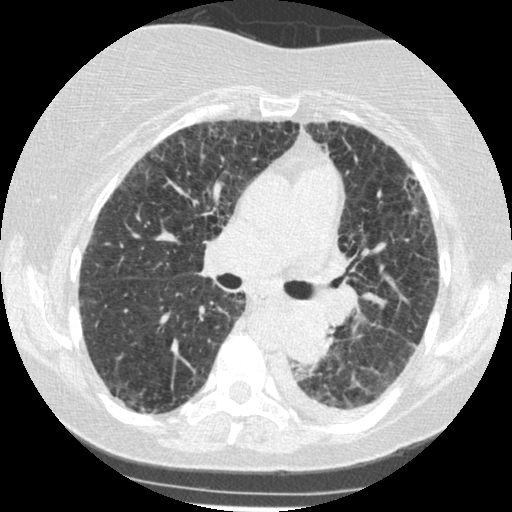
Chest CT (low-dose screening protocol), one axial image, third screening round (two years after baseline), lung window (W 1500 / L -600 HU), 120 kVp, slice 190 of 341 in the series. Female participant, aged 60 years at enrolment. Former smoker at enrolment.
- Expert reader's lesion annotation, bounding box [x1, y1, x2, y2] px = [269, 308, 341, 374].
- Reader record for this screening exam (exam-level; its link to the box is not recorded): non-calcified nodule or mass ≥4 mm, left lower lobe, 54 × 38 mm, smooth margins, soft tissue attenuation, pre-existing on the prior screen: yes; interval growth: yes.
- Official screen result: positive, other.
- Later outcome: lung cancer diagnosed 15 days after this screen — small cell carcinoma, NOS, left lower lobe, undifferentiated (G4), stage IV (AJCC 6th edition), 69 mm at pathology.